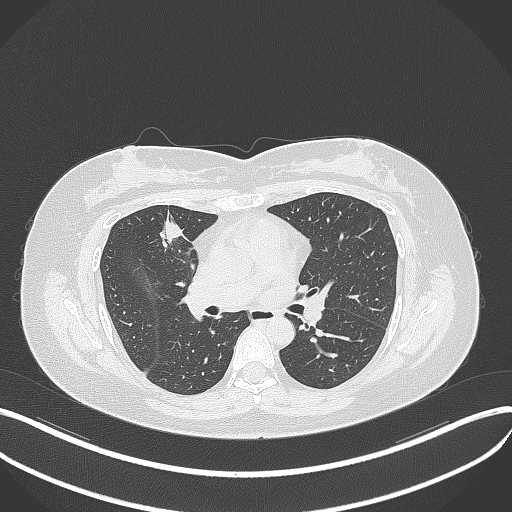
Chest CT, one axial slice; position 176 of 273 along the scan axis; lung window (W 1500 / L -600 HU); 1 mm slice thickness; 512 × 512 image matrix, field of view 400 × 400 mm. Patient: female, 42 years. Case-level facts recorded for this patient, not image findings: clinical TNM (as recorded): T1b N0 M0.
Outlined on this slice (bounding box drawn by a radiologist):
- lung tumour (recorded histology: adenocarcinoma): bounding box <153,211,191,252> (left, top, right, bottom; pixels)